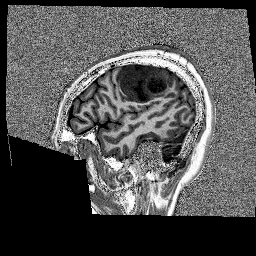
Brain MRI from a brain-tumour surgery series, one sagittal slice. Slice 41 of 176 in the series (ordered by position). 1 mm slice thickness. 256 × 256 image matrix. From the clinical record (not read from this slice): histopathology: Glioblastoma; WHO grade: 4; IDH mutation: no.
Outlined on this slice (outlined manually by an expert reader):
- tumour: box from (x=118, y=63) to (x=175, y=102) px